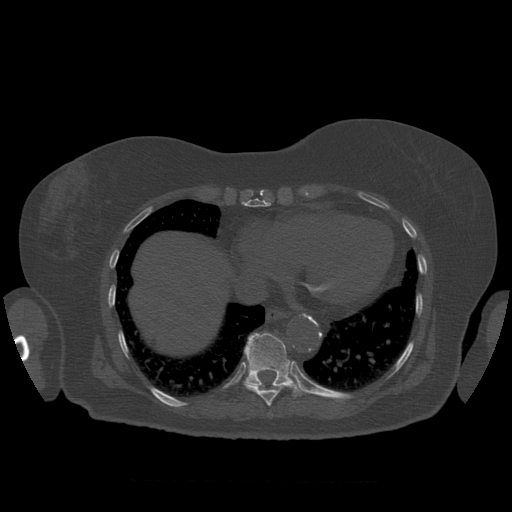
CT including the spine, one axial slice; position 350 of 399 along the scan axis; bone window (W 1800 / L 400 HU); 1.25 mm slice thickness; 512 × 512 image matrix. Patient age 81 years. Case-level facts recorded for this patient, not image findings: primary cancer: renal; vertebrae with lytic lesions (as recorded): L1.
Outlined on this slice (semi-automatic segmentation, software-assisted and operator-edited):
- T10 vertebra: bounding box [x1, y1, x2, y2] px = [245, 333, 305, 397]
- T9 vertebra: [244, 378, 284, 406]